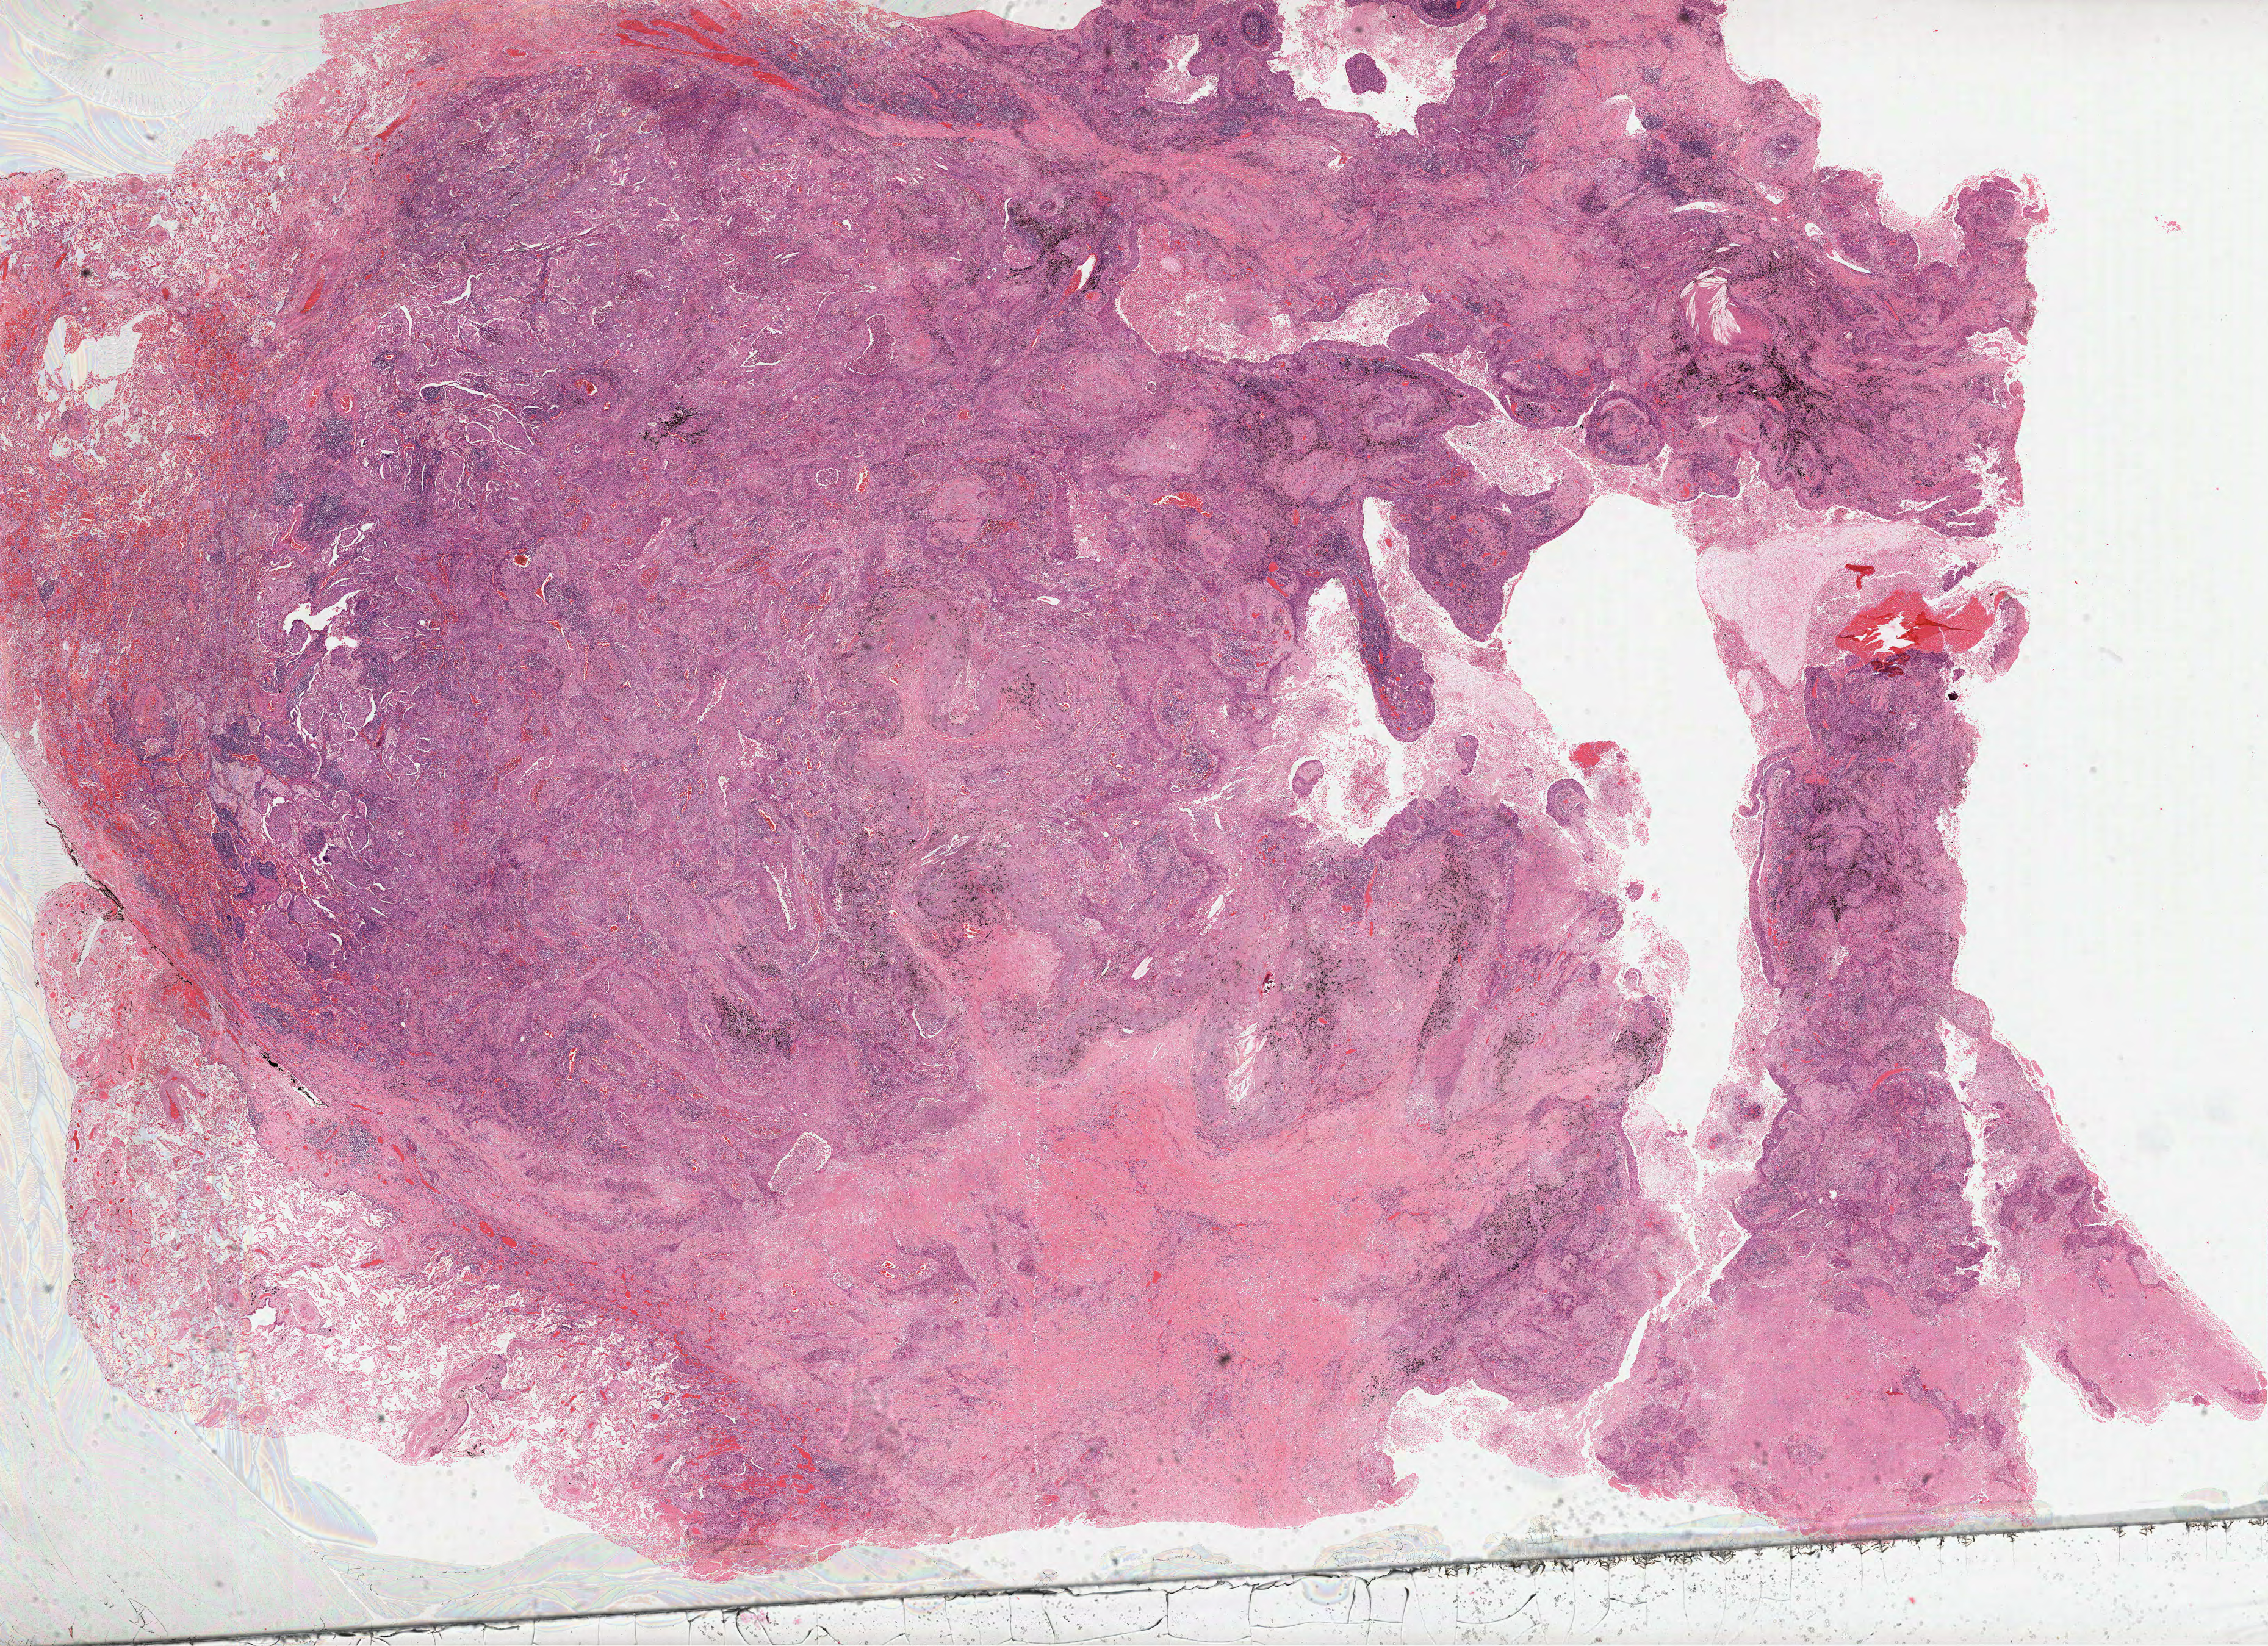
Digitized H&E tissue section (whole slide) — whole scanned area (about 30.0 x 21.8 mm, acquisition: 40x scan) shown as a low-resolution overview; formalin-fixed paraffin-embedded (FFPE) diagnostic section; lung, primary tumour sample. Male patient; age at initial diagnosis 76 years.
AJCC pathologic stage: IIIA (6th edition). Histologic diagnosis: Squamous cell carcinoma, NOS (upper lobe, lung).